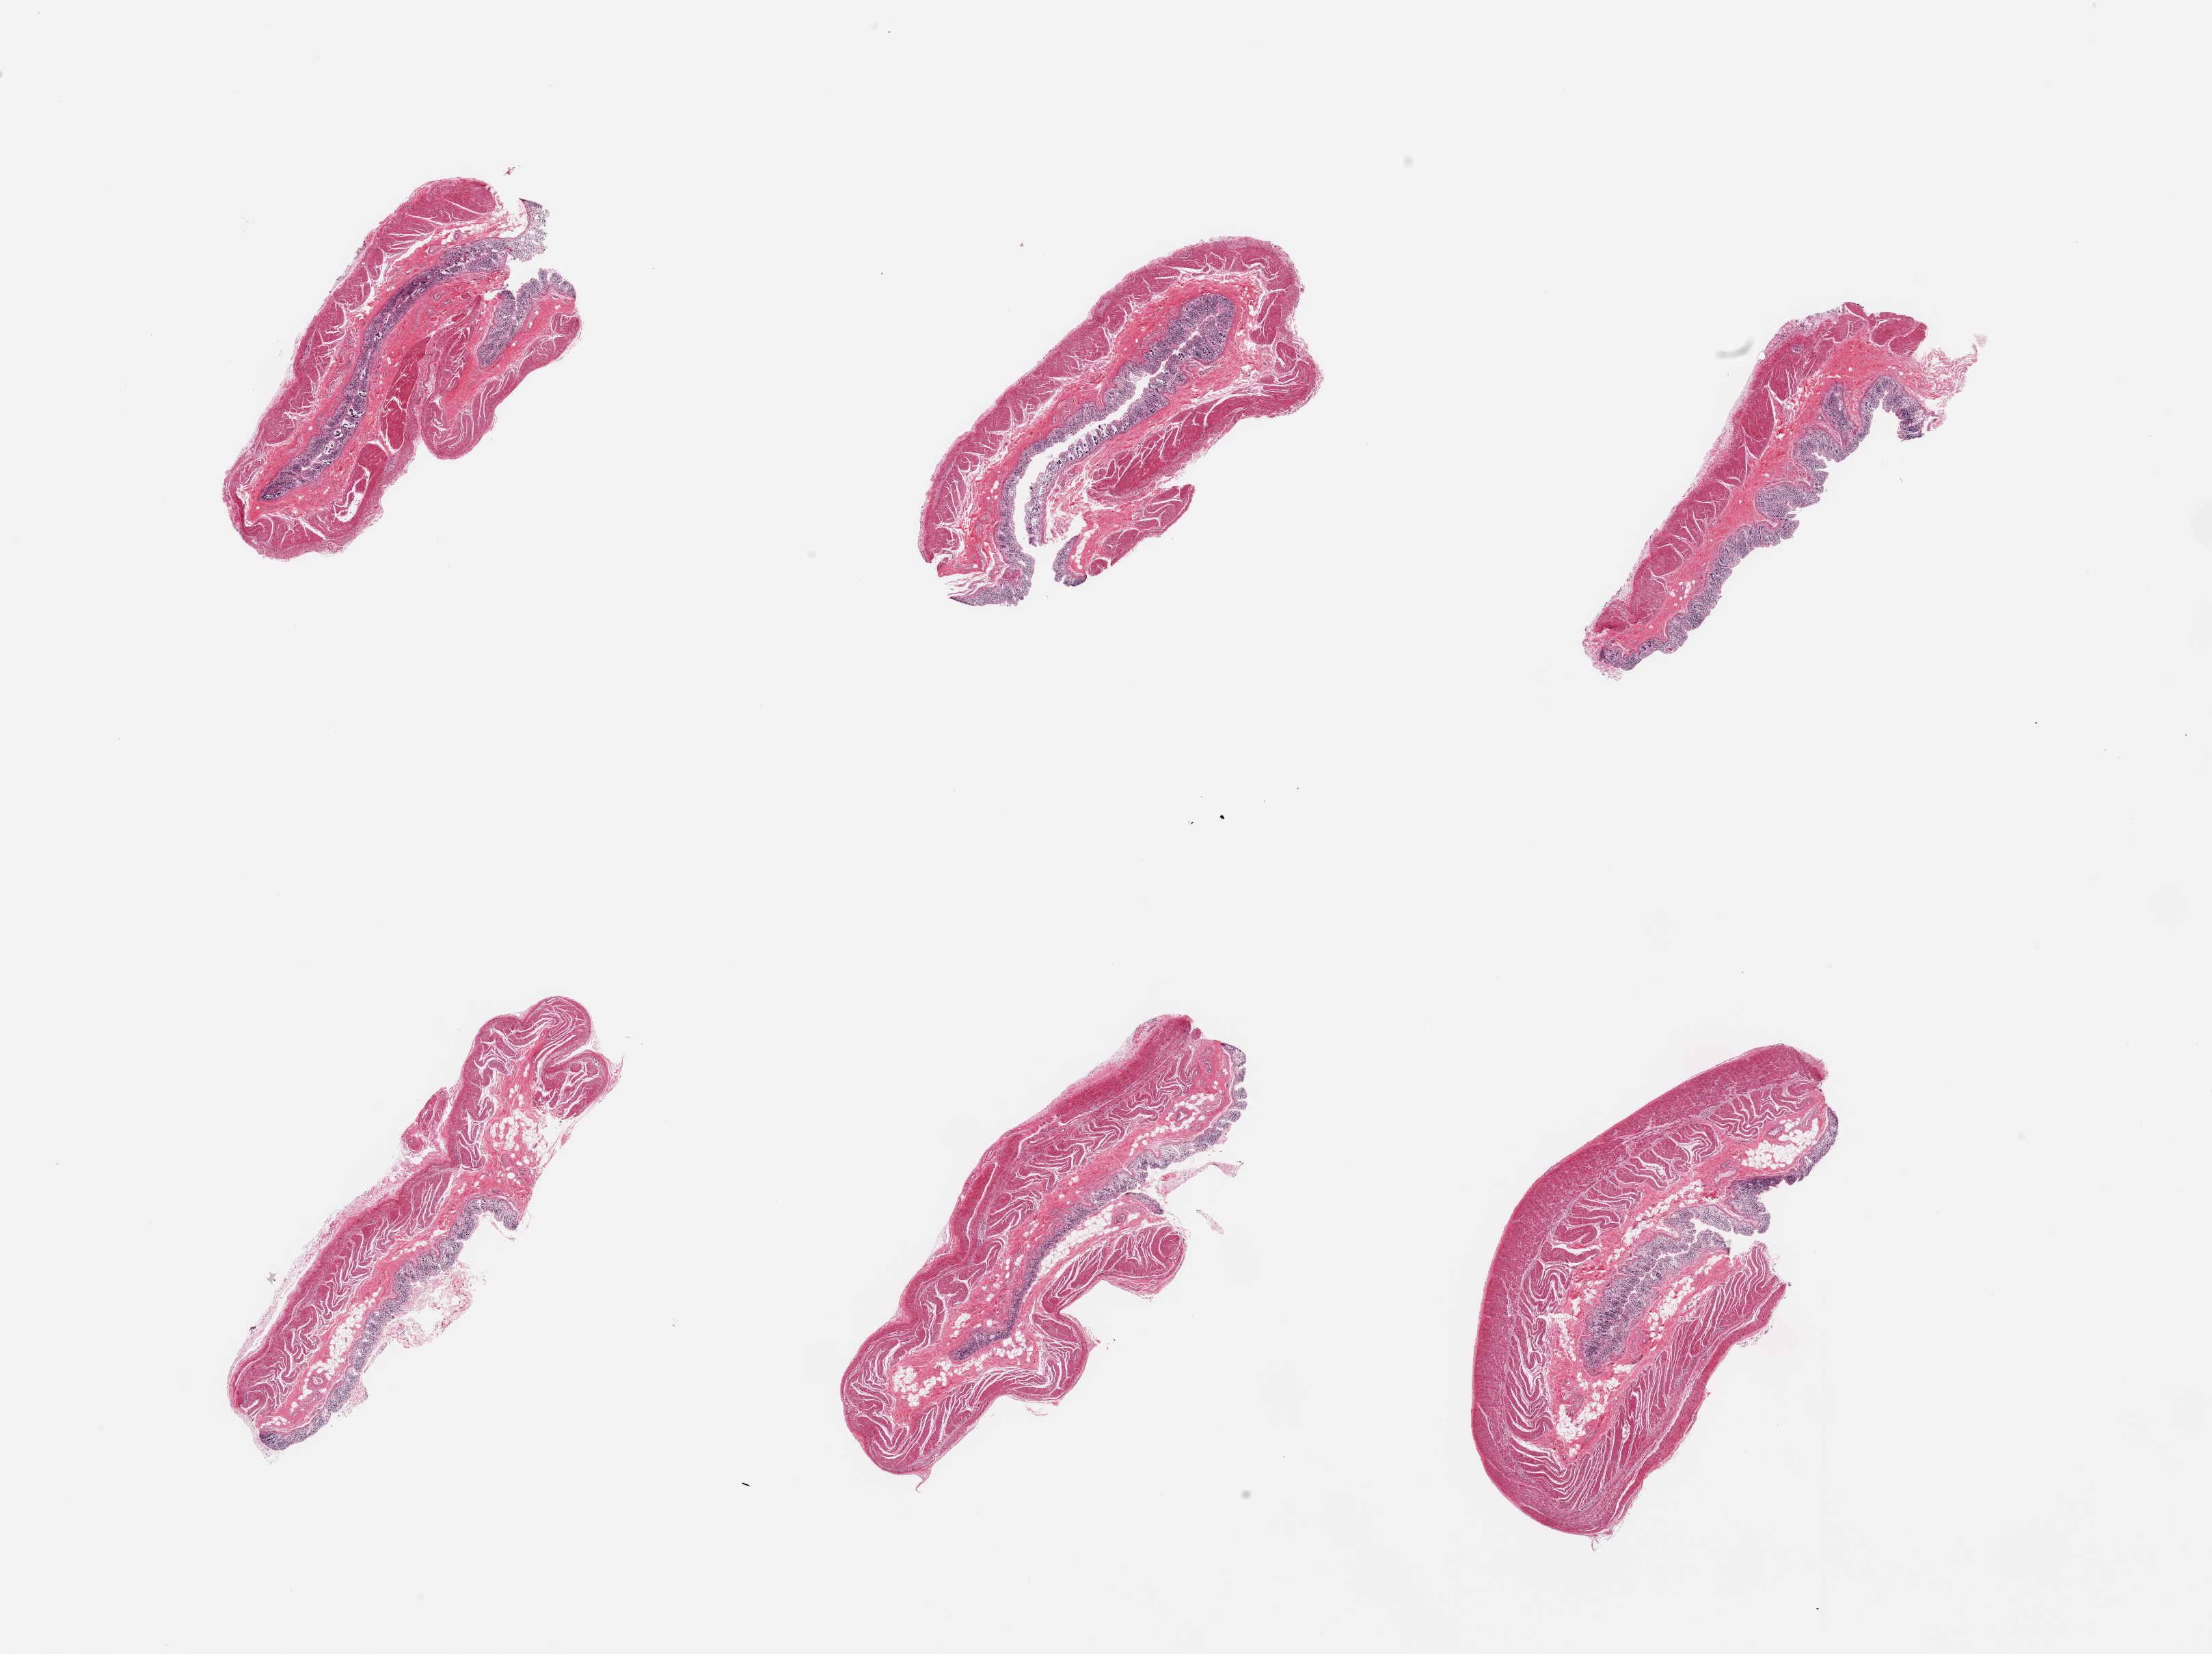
Whole-slide image, hematoxylin and eosin (H&E) stain — whole scanned area (about 25.6 x 19.1 mm) shown as a low-resolution overview; PAXgene-fixed, paraffin-embedded tissue; section of transverse colon (target tissue); tissue donor sample. Donor: male.
Pathologist's review note for this sample: 6 pieces, target muscosa up to ~0.3mm, 10-20% thickness, with complete glandular mucosal autolysis, lamina propria intact.